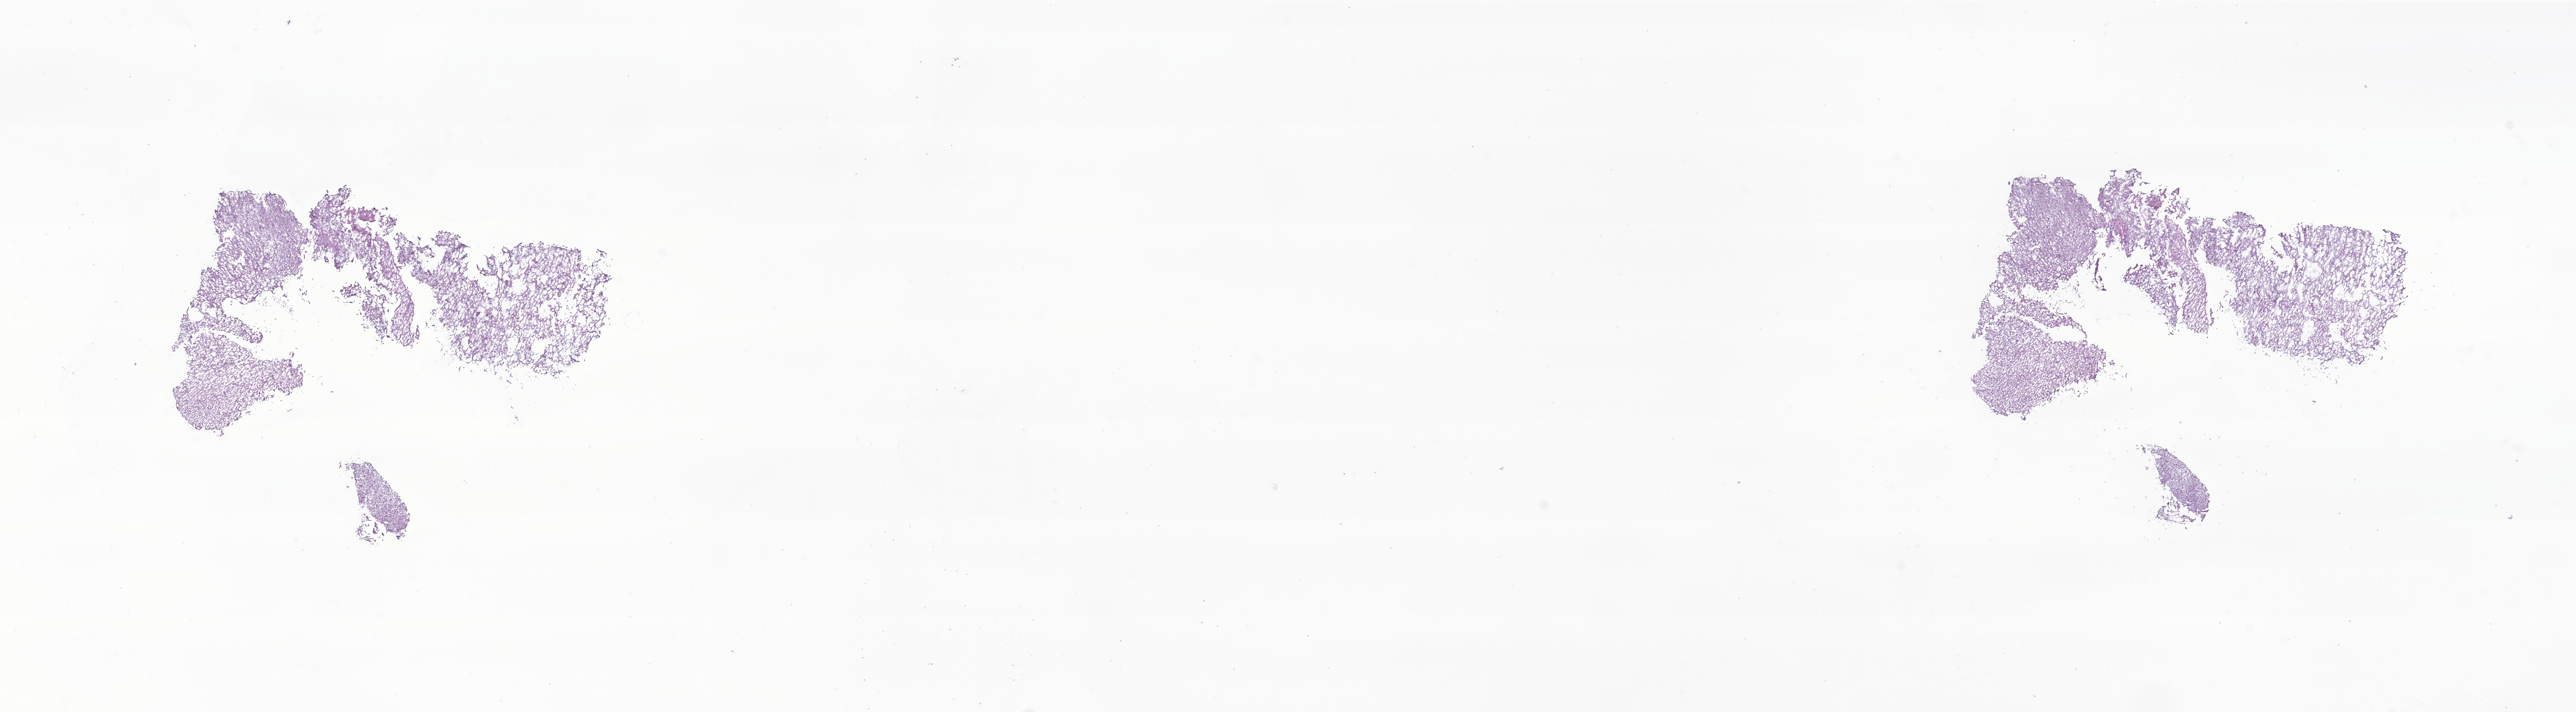
H&E whole-slide image of tumor tissue from the cerebellum — low-resolution overview of the scanned area, about 28.0 x 7.7 mm, cryosection (OCT / tissue freezing medium). Male patient, age 91 months (7 years 7 months).
Recorded diagnosis: Pilocytic astrocytoma.